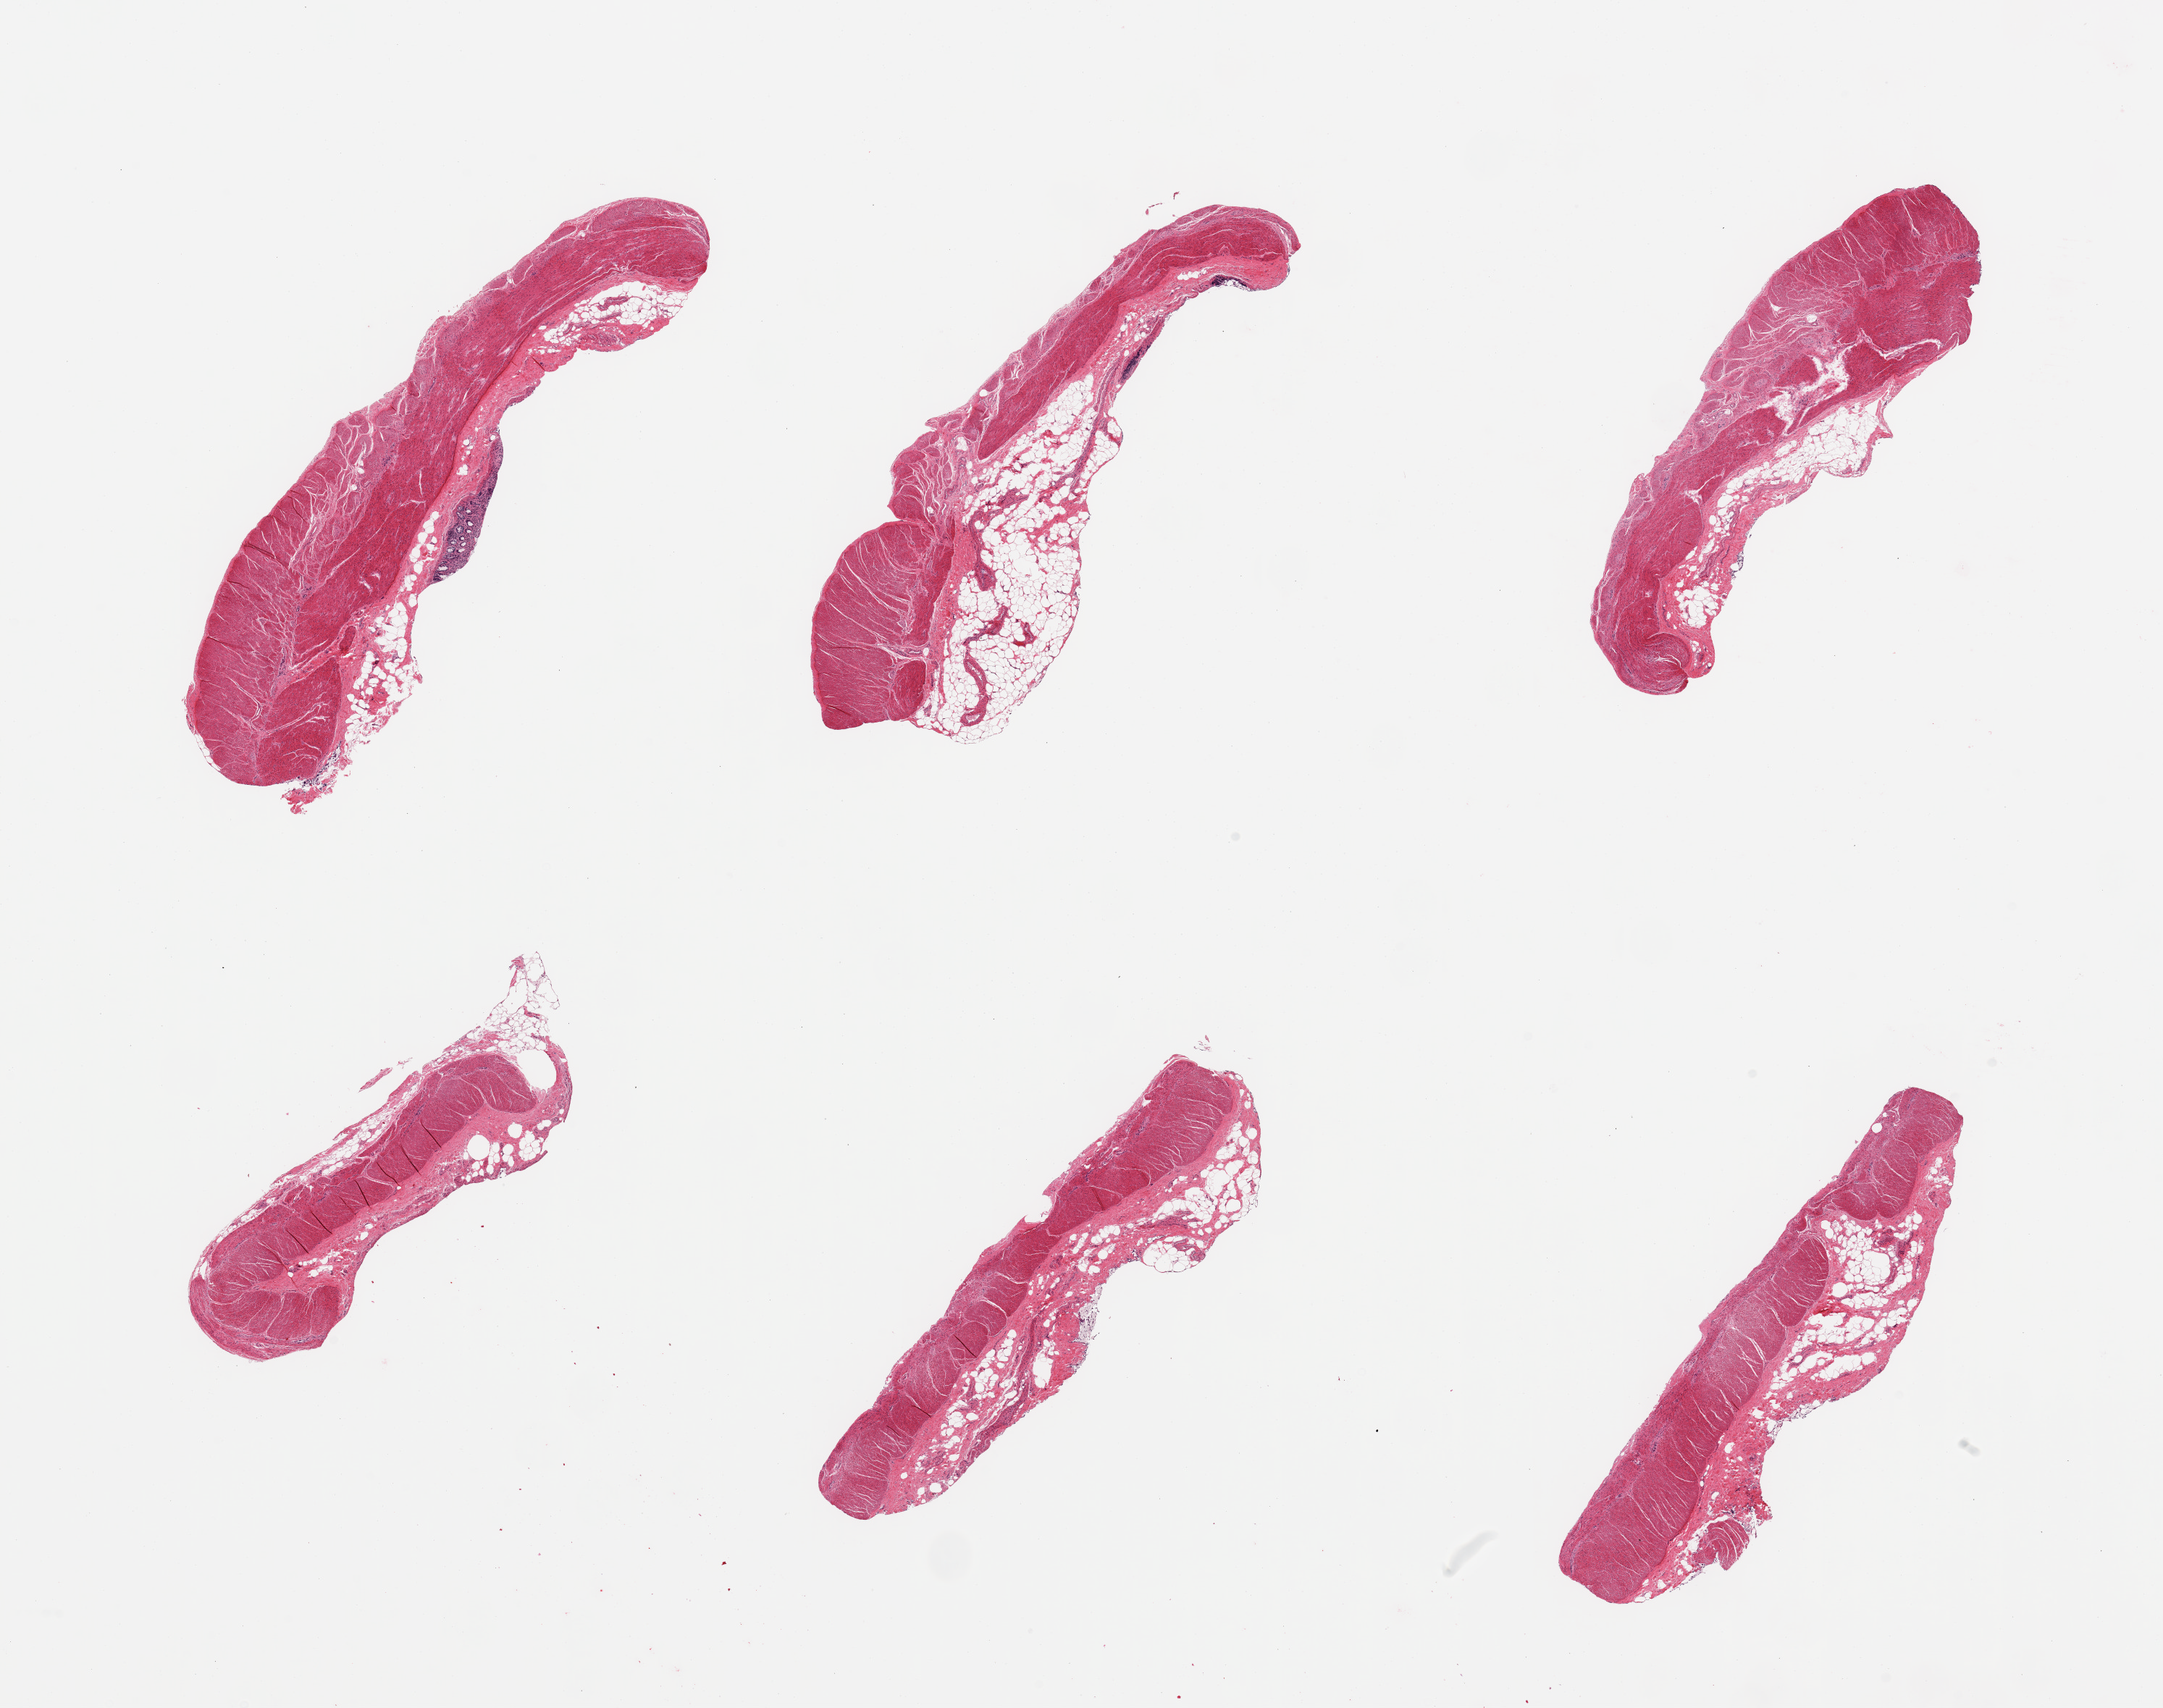
Digitized haematoxylin and eosin-stained section, shown as a low-resolution overview of the whole scanned area (about 23.6 x 18.7 mm, from a 20x scan). PAXgene-fixed paraffin-embedded (PFPE) section. Target tissue: sigmoid colon. Tissue donor sample. Male donor.
* pathologist's review note for this sample: 6 pieces, focal adherent fat